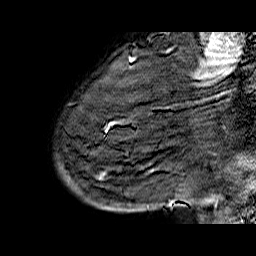
Breast MRI (dynamic contrast-enhanced), one sagittal slice; dynamic contrast-enhanced series, time point 2 of 6 at this slice position (early post-contrast); 1.5 T; TE 6.5 ms, TR 32.9 ms; 256 × 256 image matrix, field of view 200 × 200 mm. Female patient. Case-level facts recorded for this patient, not image findings: setting: breast cancer imaged before/during neoadjuvant chemotherapy; receptor status: HR-positive, HER2-negative.
Outlined on this slice (semi-automatically segmented with operator editing):
- analysis volume of interest (the breast-tissue region the enhancement analysis was run in; not a lesion): box from (x=56, y=74) to (x=176, y=210) px
- tumour enhancement mask (voxels above the 100 % enhancement threshold inside the analysis volume of interest): (x=169, y=202)–(x=172, y=206)